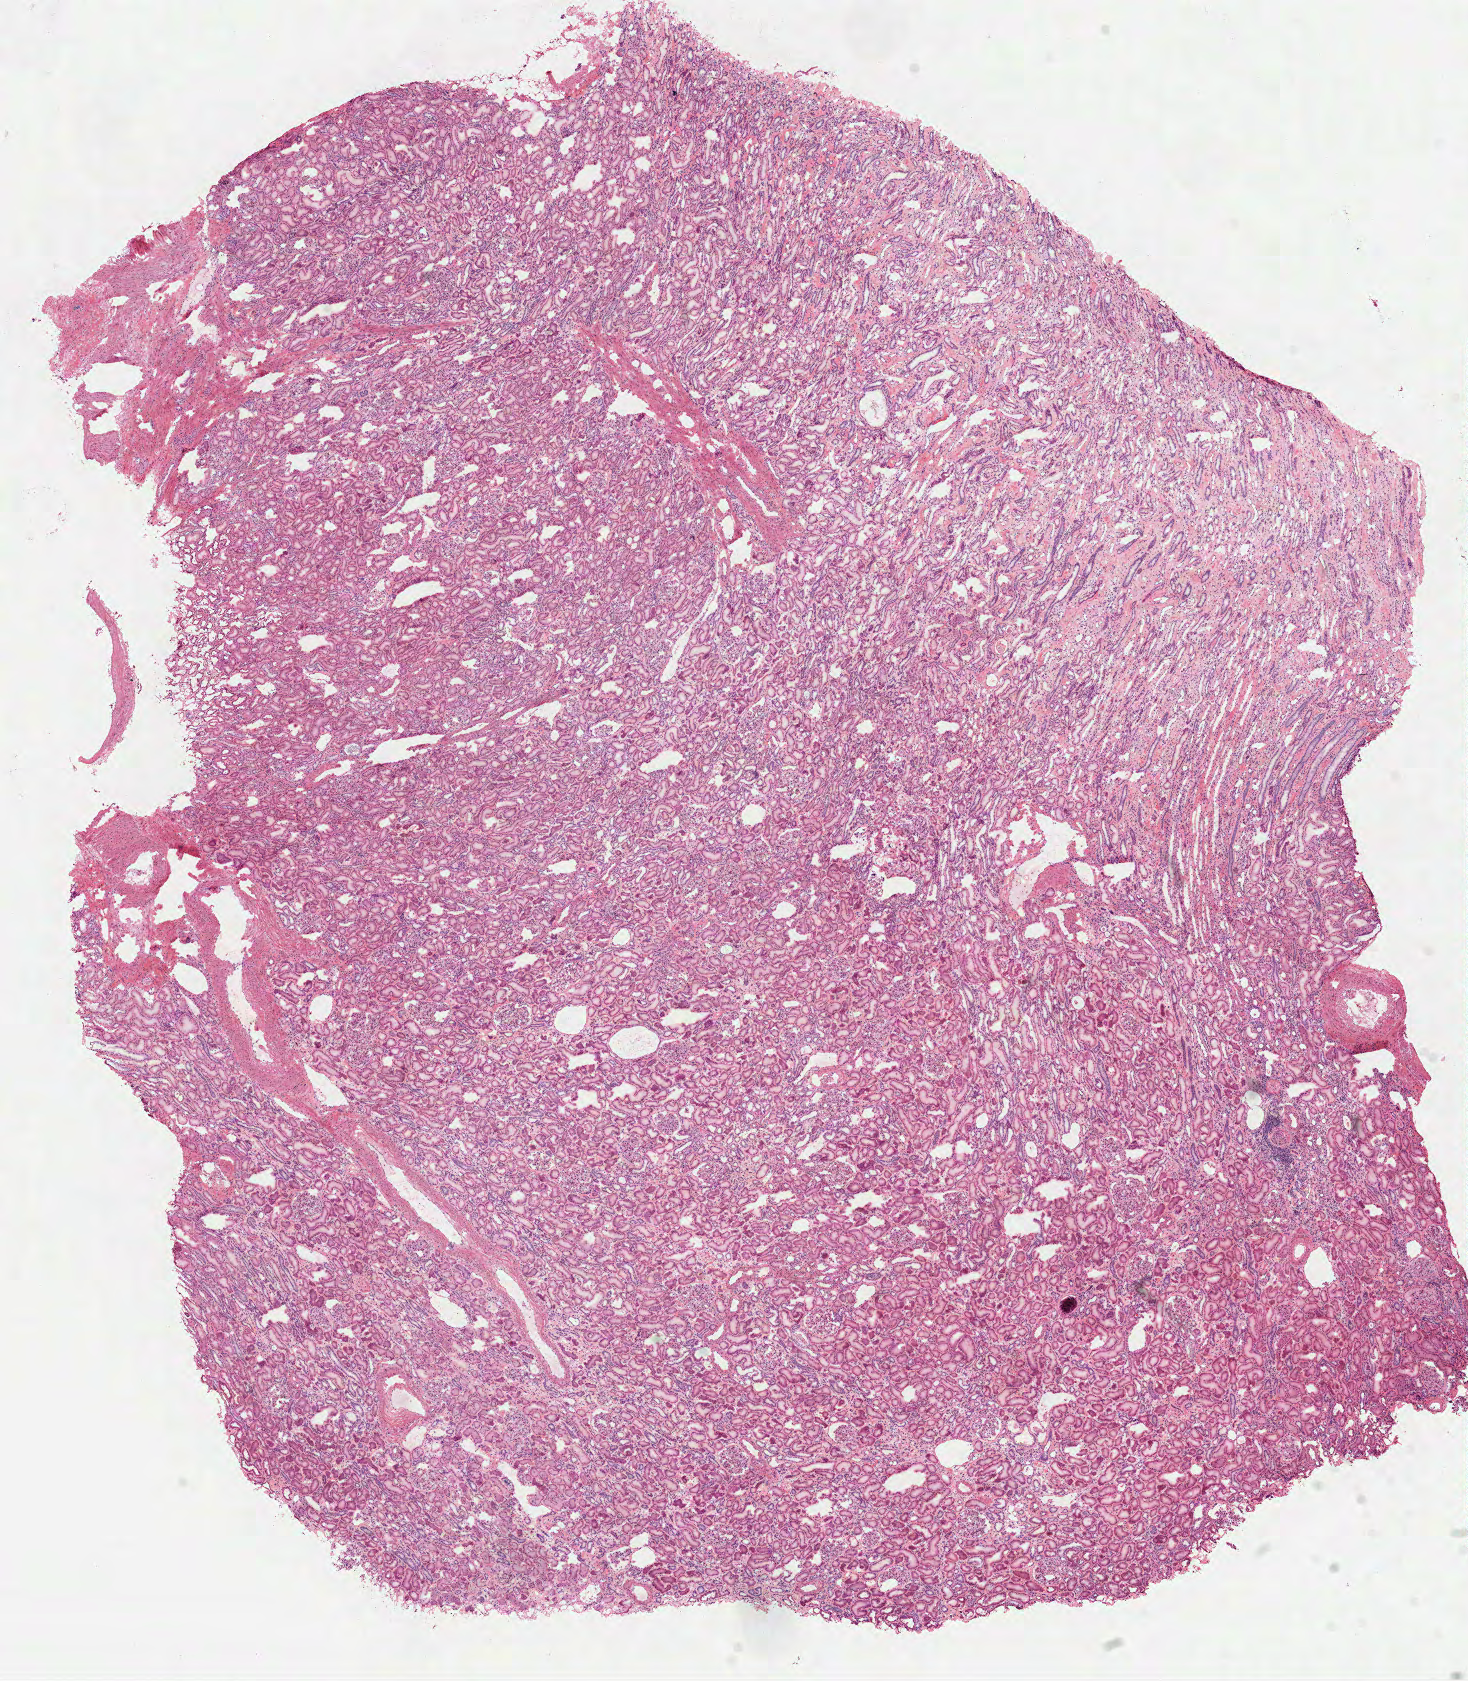
H&E whole-slide image — a low-resolution overview of the entire scanned area, about 11.8 x 13.6 mm. Frozen section from the top of the tissue portion. Sample: solid tissue normal (non-tumour tissue), kidney. Patient: male, age at initial diagnosis 74 years.
This section: solid tissue normal (non-tumour) sample from the same patient. Patient diagnosis: Papillary adenocarcinoma, NOS.